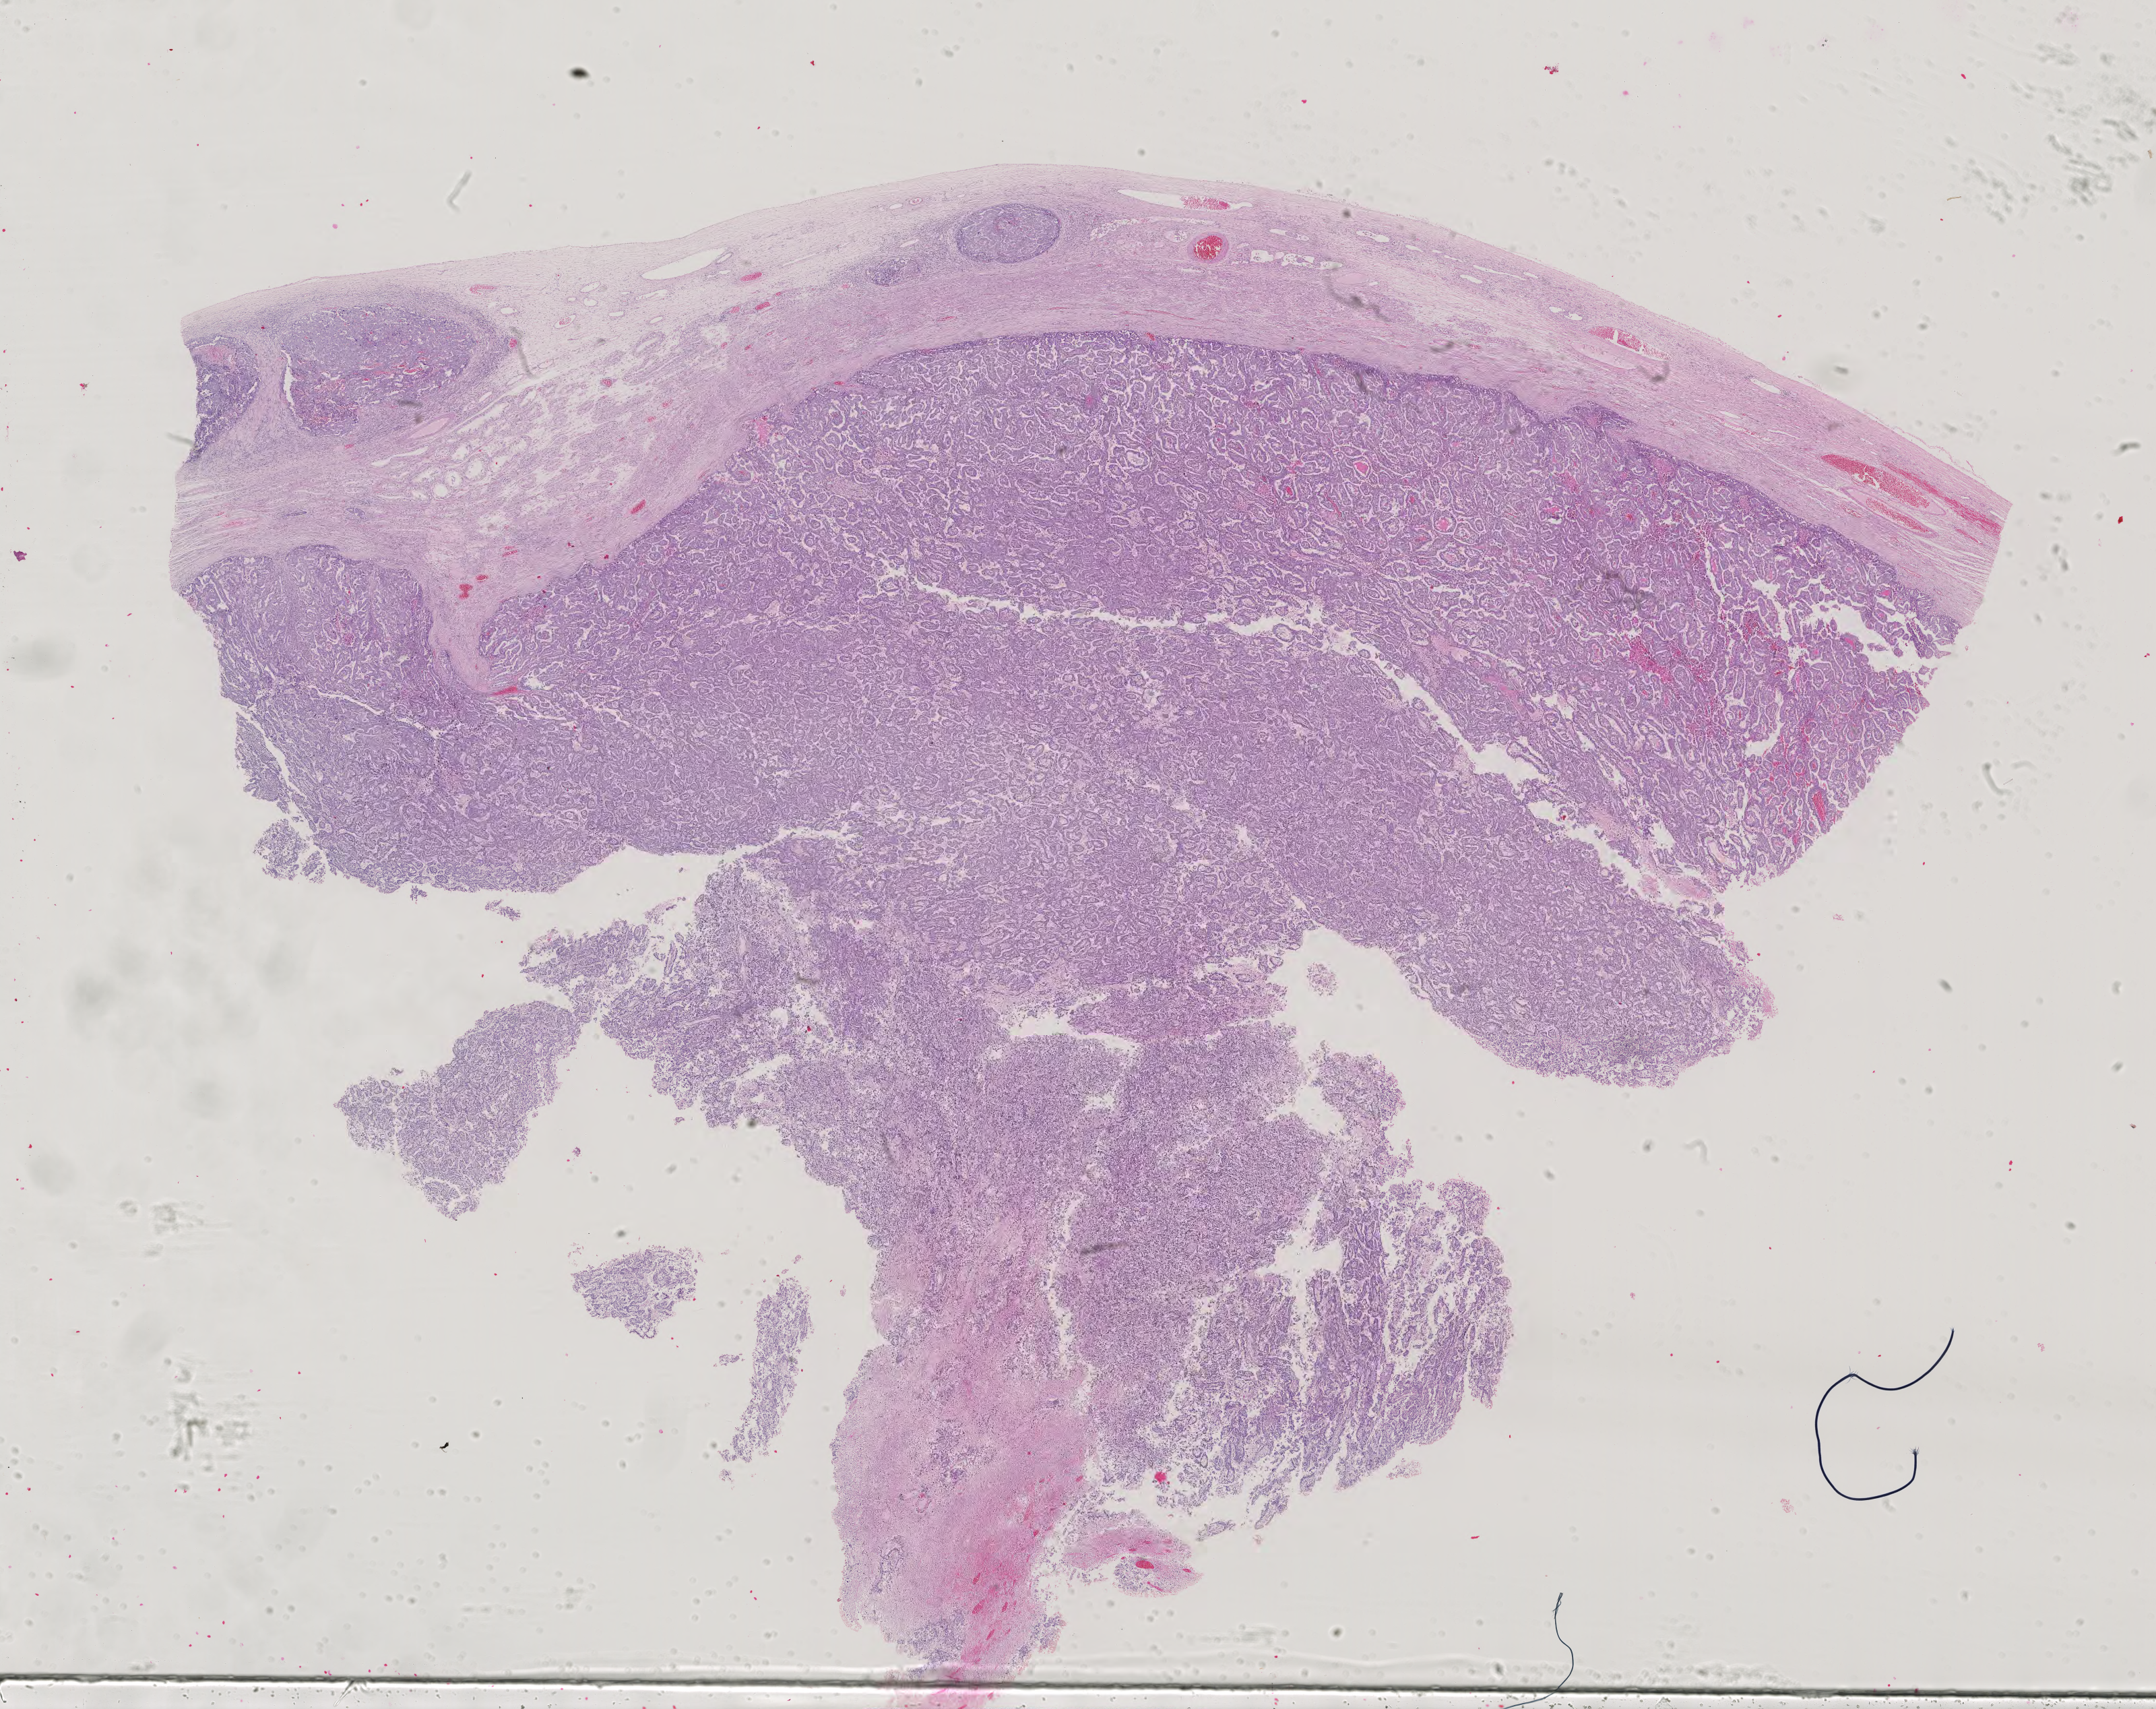
Whole-slide histology image, H&E-stained — a low-resolution overview of the entire scanned area, about 23.3 x 18.5 mm. Male patient.
• specimen: formalin-fixed paraffin-embedded (FFPE) diagnostic section; sample: primary tumour, testis